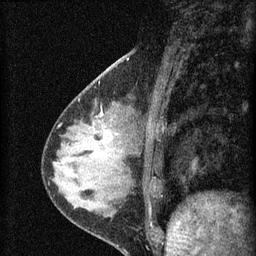
Breast MRI (dynamic contrast-enhanced), one sagittal slice; slice 20 of 60 in the series (ordered by position); dynamic contrast-enhanced series, image 2 of 4 at this slice position (ordered by acquisition); 1.5 T; TE 4.2 ms, TR 8.2 ms; 256 × 256 image matrix, field of view 180 × 180 mm. Patient: female, 37 years.
Outlined on this slice (semi-automatic segmentation, software-assisted and operator-edited):
- analysis volume of interest (the breast-tissue region the enhancement analysis was run in; not a lesion): bounding box <77,116,127,175> (left, top, right, bottom; pixels)
- tumour enhancement mask (voxels above the 70 % enhancement threshold inside the analysis volume of interest): <106,131,111,135>